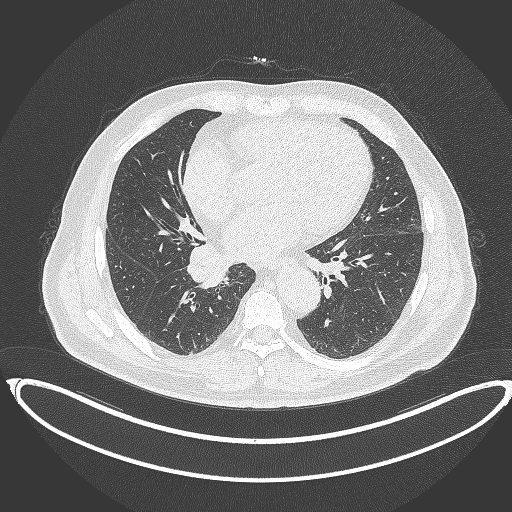
Chest CT, one axial slice; slice 183 of 387 in the series (ordered by position); reconstruction kernel B70f; lung window (W 1500 / L -600 HU); 1 mm slice thickness; 512 × 512 image matrix, field of view 448 × 448 mm. Patient: male, 61 years. Case-level facts recorded for this patient, not image findings: clinical TNM (as recorded): T1b N1 M0.
Annotated regions visible in this slice (bounding box drawn by a radiologist):
- lung tumour (recorded histology: squamous cell carcinoma): bounding box (x1, y1, x2, y2) in pixels: (183, 238, 228, 291)